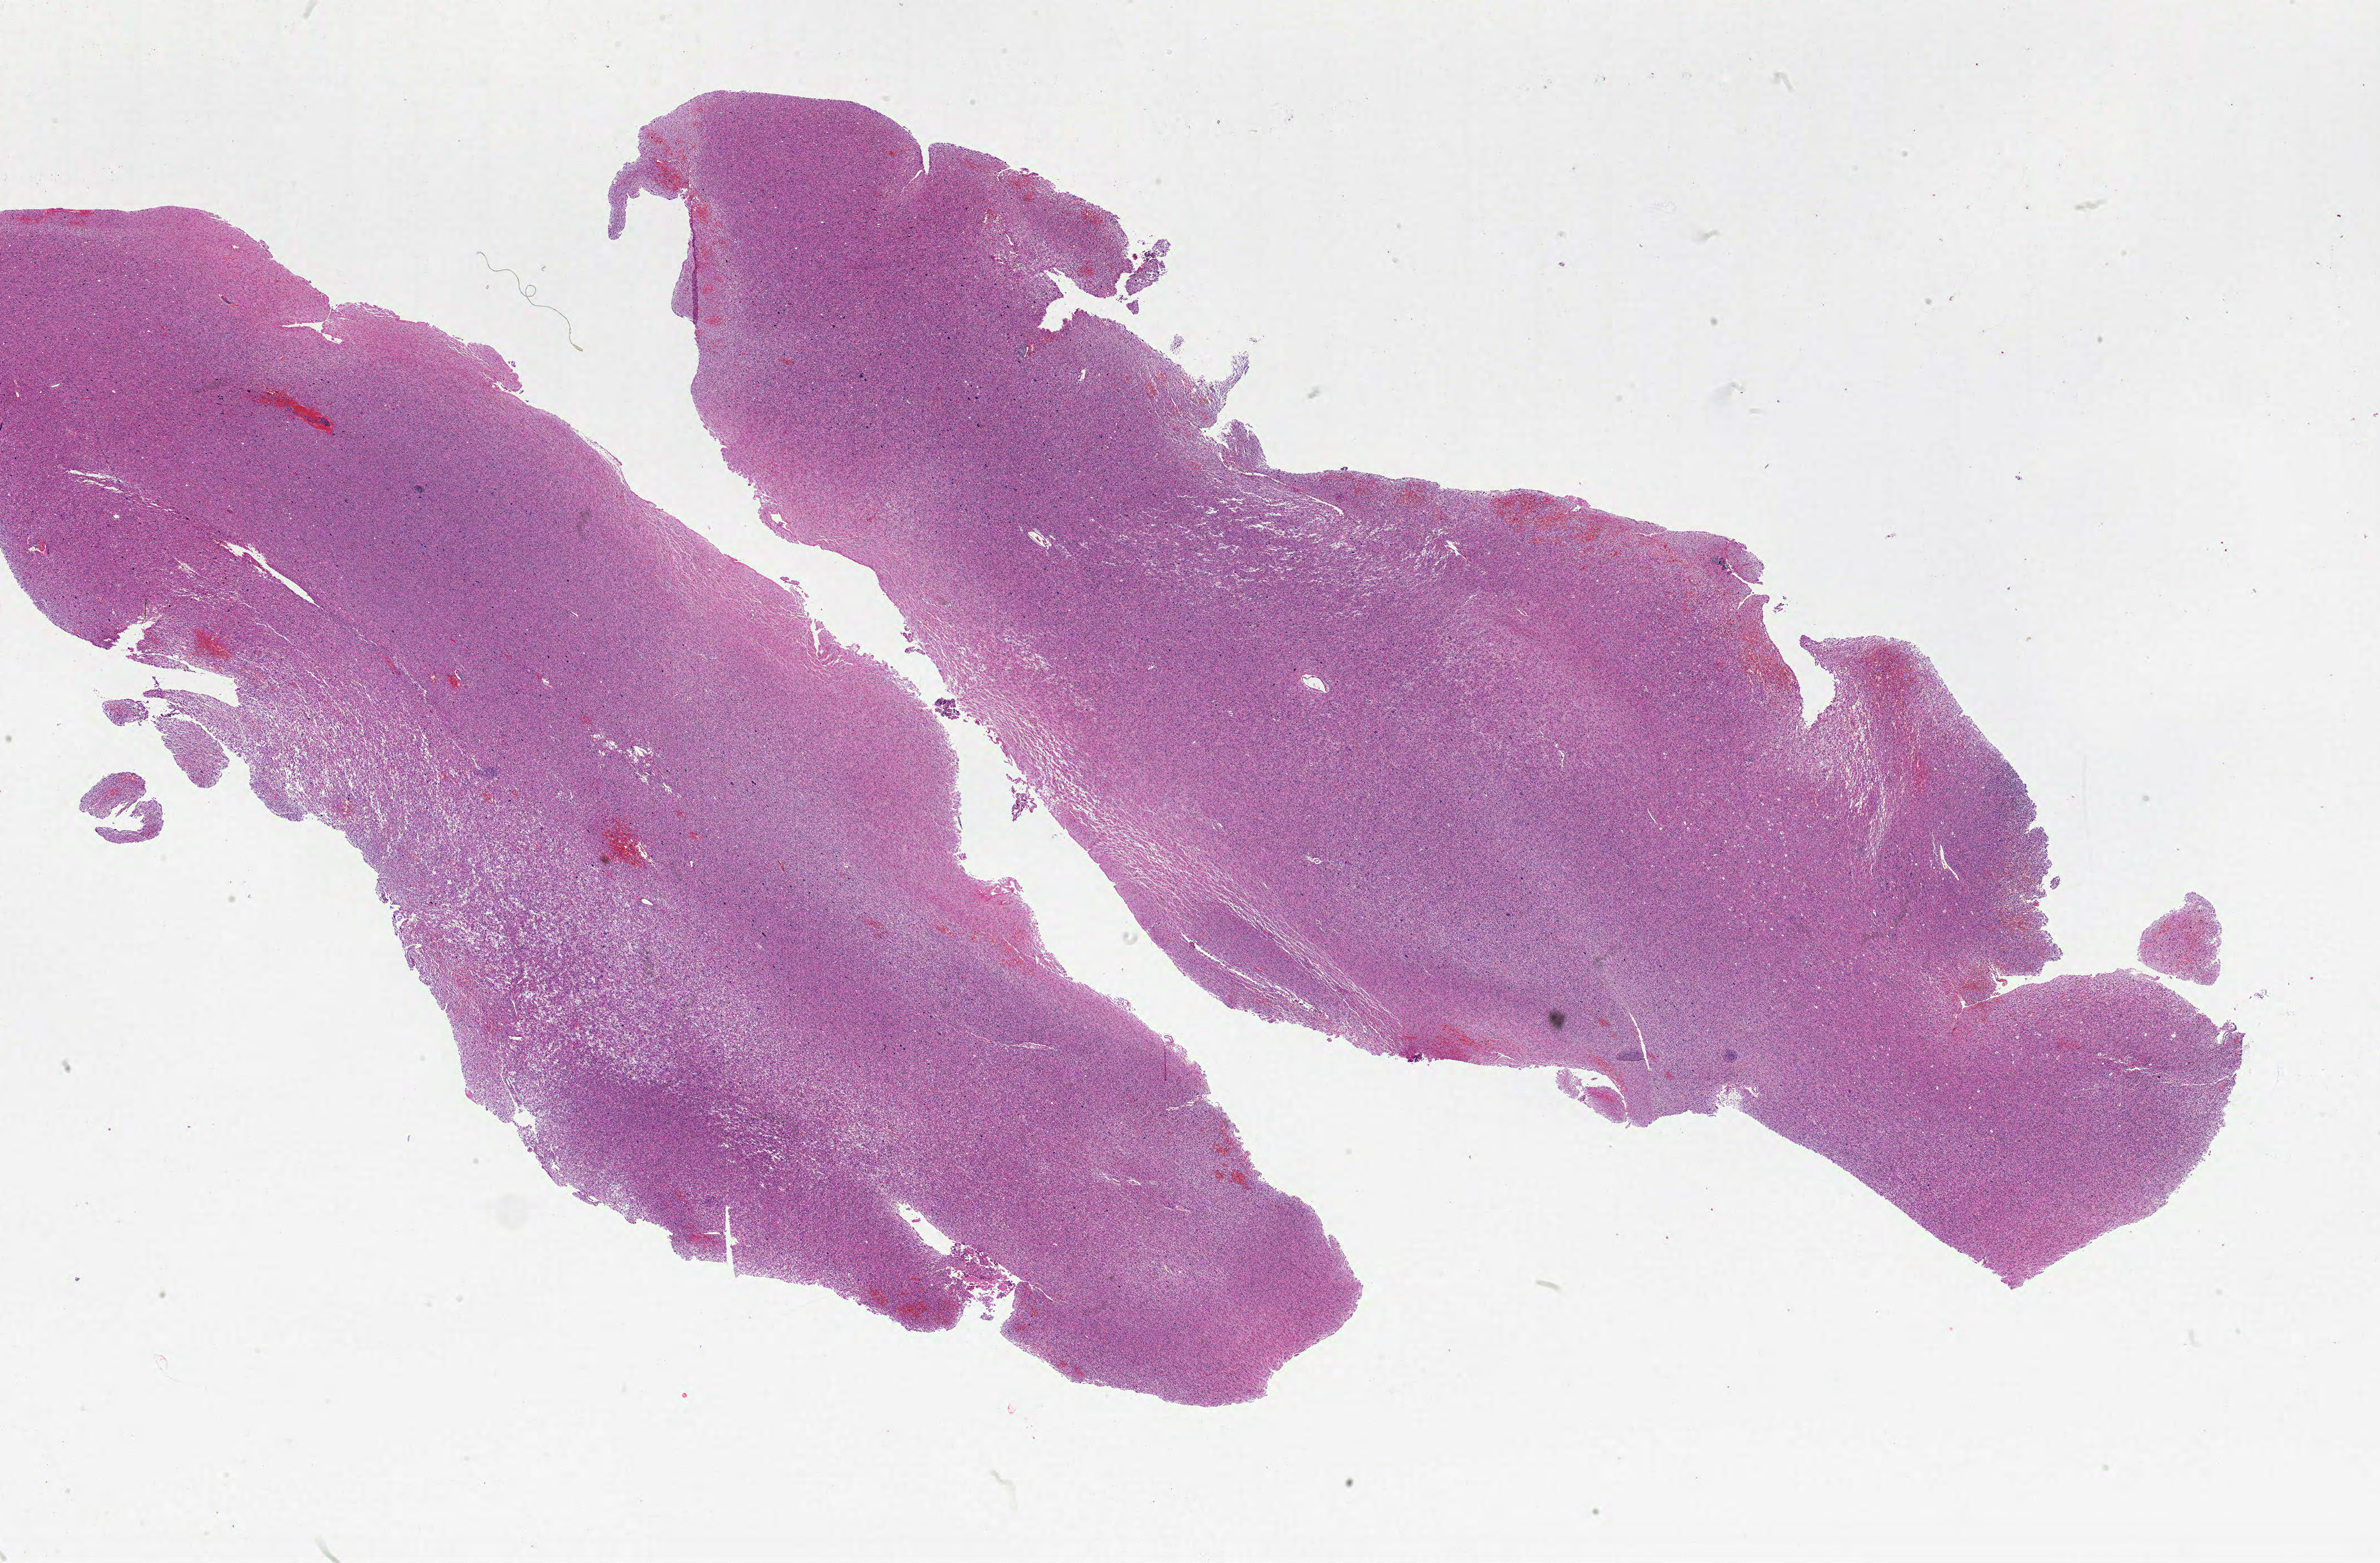
Whole-slide histology image, Hematoxylin and eosin (H&E) stained — a low-resolution overview of the entire scanned area, about 34.0 x 22.3 mm; formalin-fixed paraffin-embedded (FFPE) diagnostic section; sample: primary tumour, brain. Patient: male, age at initial diagnosis 63 years.
Diagnosis: Glioblastoma.